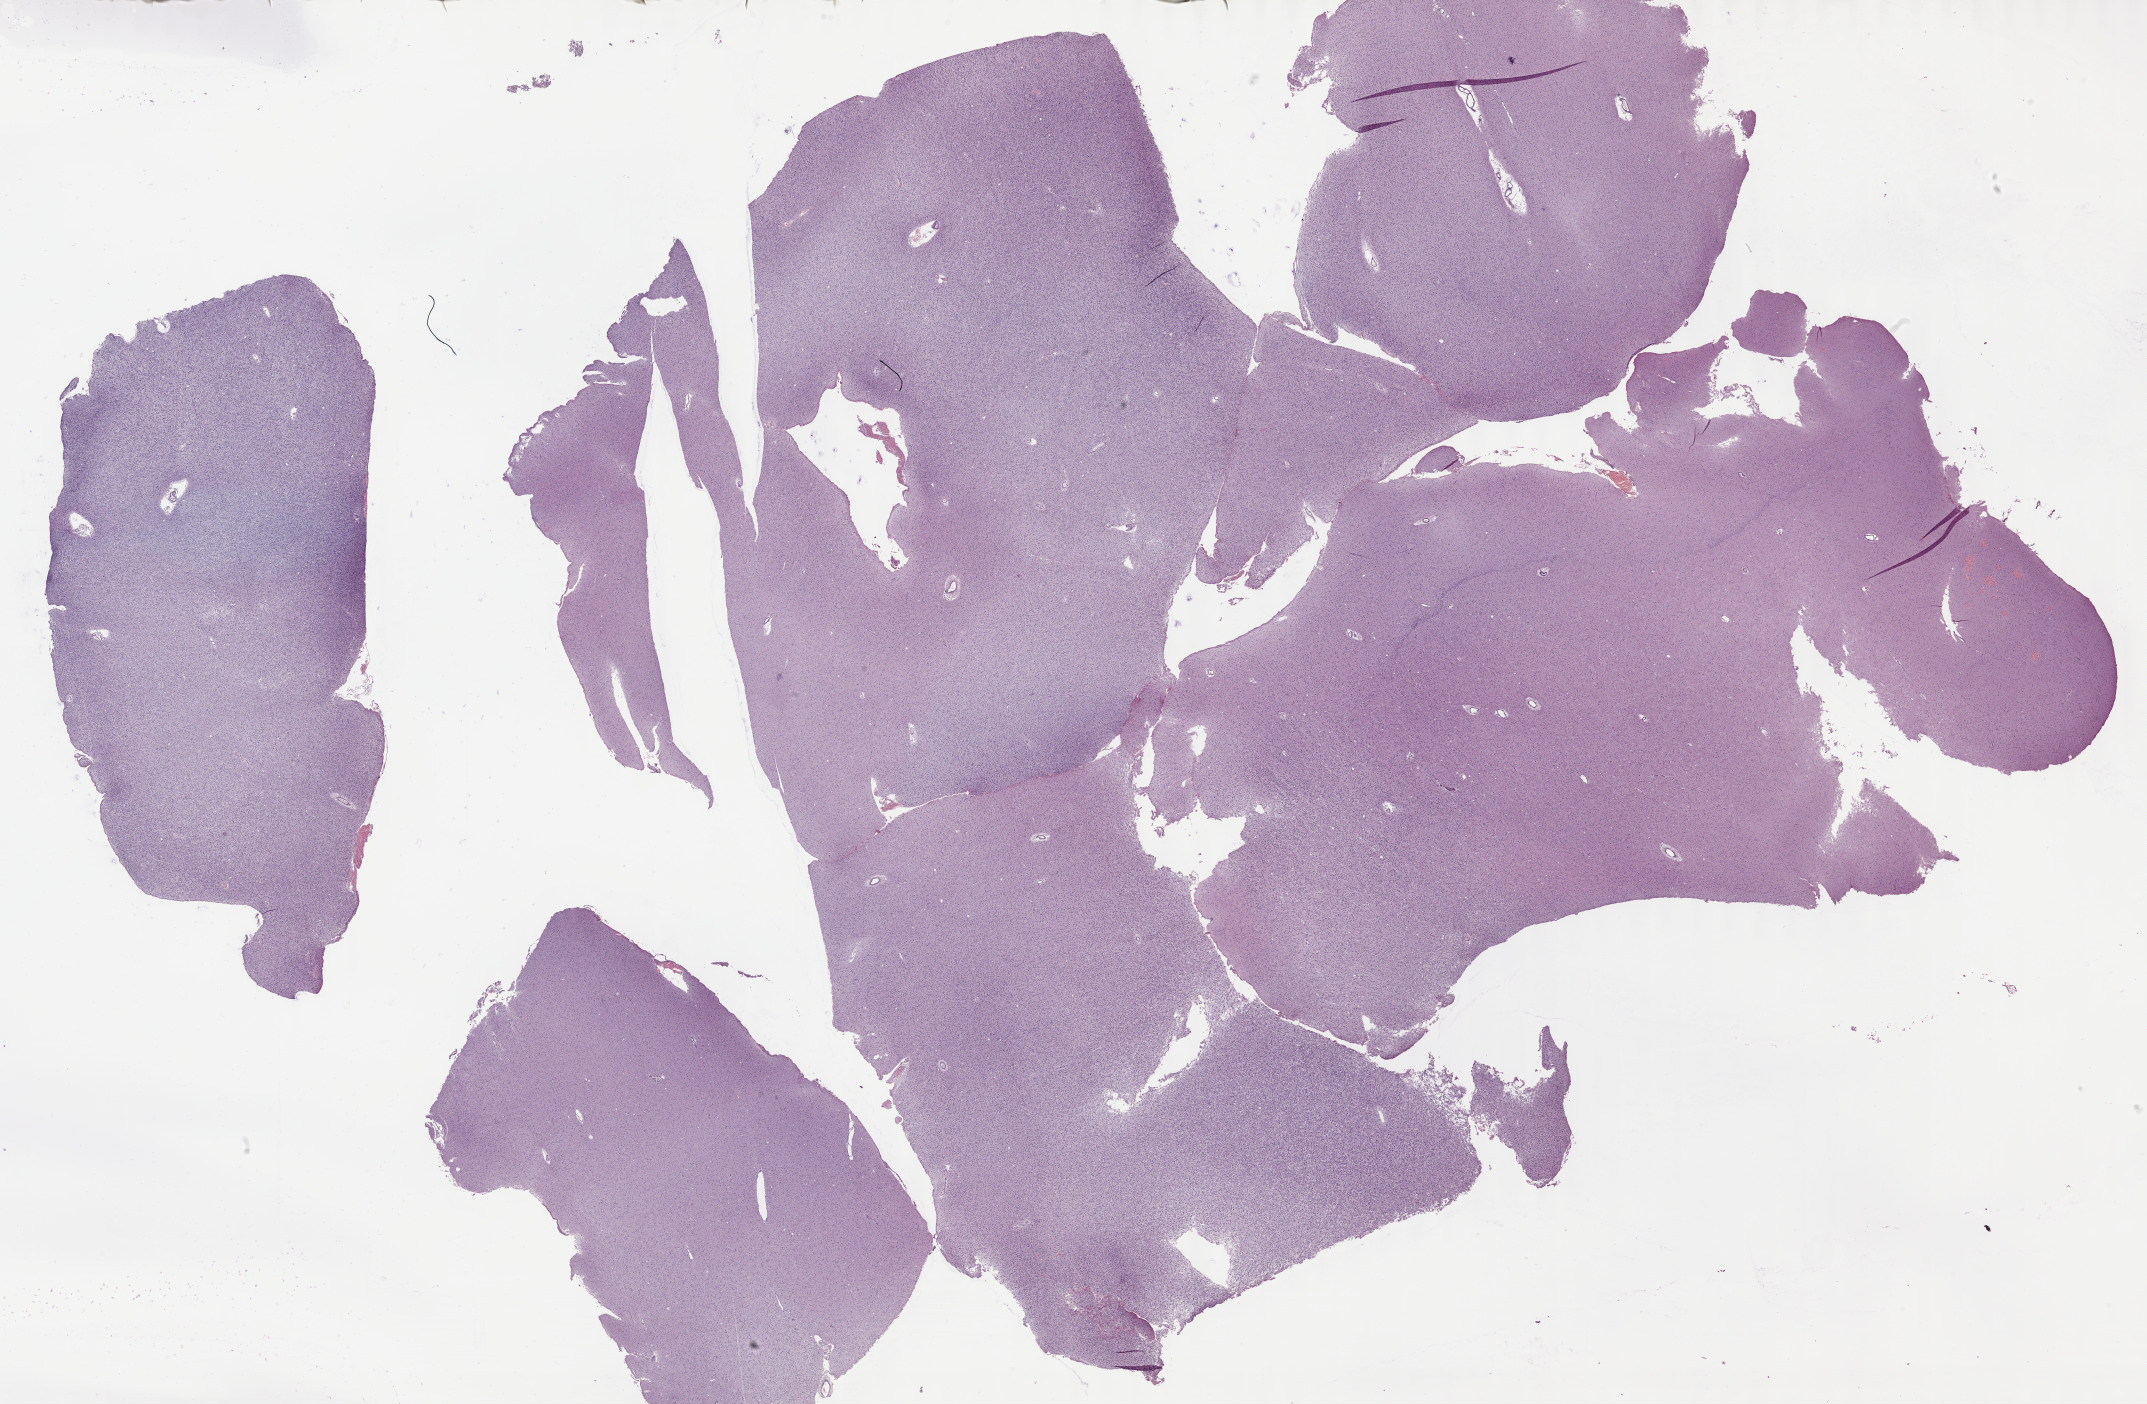
H&E-stained whole-slide image, low-resolution overview of the scanned area, about 34.7 x 22.7 mm (slide scanned at 40x), FFPE section, sample: primary tumour, brain. Patient: female, age at initial diagnosis 38 years. Histologic grade: G2 (moderately differentiated).
Pathologic diagnosis: Astrocytoma, NOS (cerebrum).